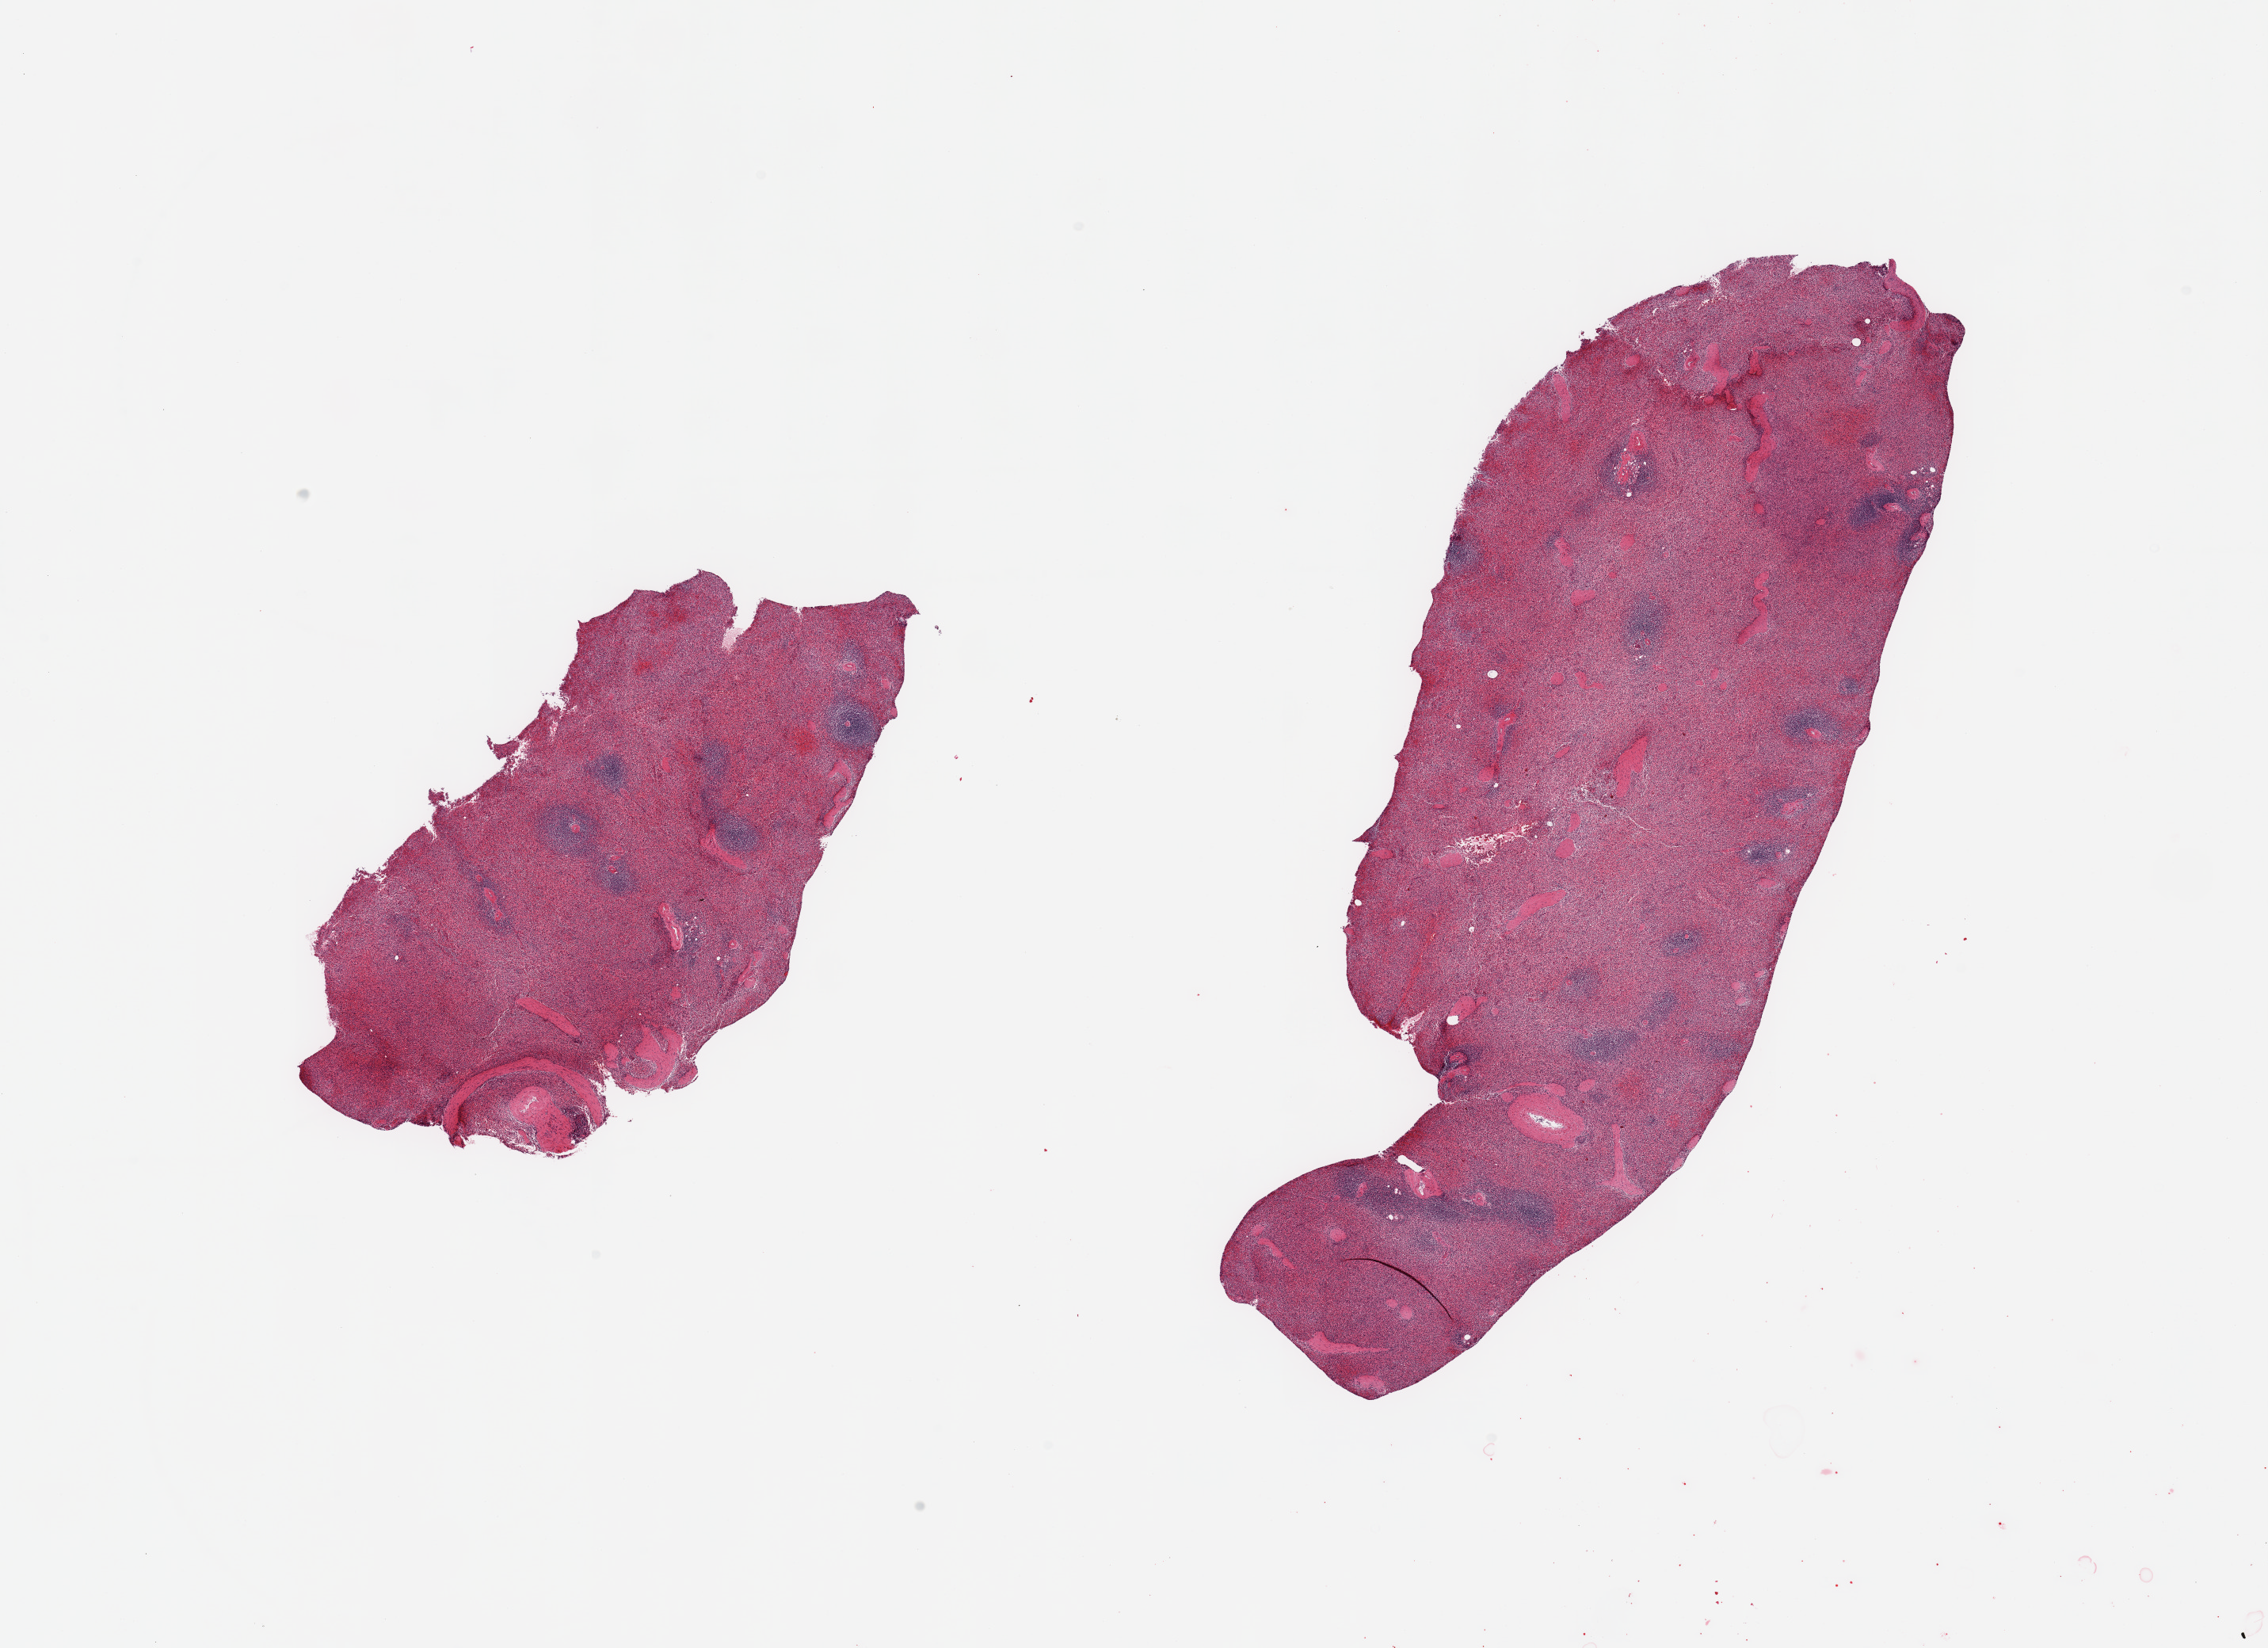
Digitized haematoxylin and eosin-stained section — a low-resolution overview of the entire scanned area, about 22.6 x 16.4 mm (slide scanned at 20x); PAXgene-fixed paraffin-embedded (PFPE) section; section of spleen (target tissue); tissue donor sample. Male donor.
Review note (as recorded): 2 pieces; minimally congested.